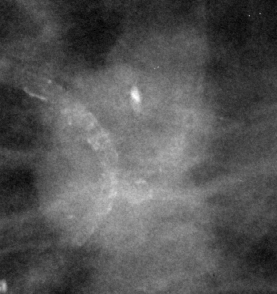
Region of interest cut from a scanned film mammogram (one marked finding), right breast, CC view, BI-RADS breast density category 3 (scale 1–4).
- Mass, shape architectural distortion, margins ill defined / spiculated; BI-RADS assessment category 4; pathology (as recorded): malignant.